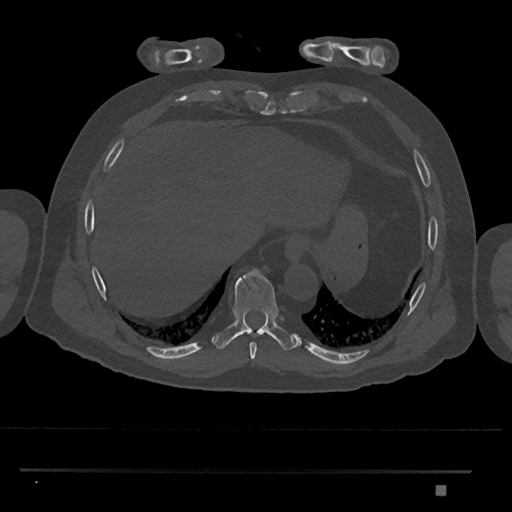
CT including the spine, one axial slice. Position 1068 of 1134 along the scan axis. Bone window (W 1800 / L 400 HU). 0.5 mm slice thickness. 512 × 512 image matrix. Patient: male, 65 years. From the clinical record (not read from this slice): primary cancer: prostate.
Structures marked on this image (semi-automatically segmented with operator editing):
- T8 vertebra: bounding box [x1, y1, x2, y2] px = [250, 342, 257, 360]
- T9 vertebra: [215, 269, 296, 351]